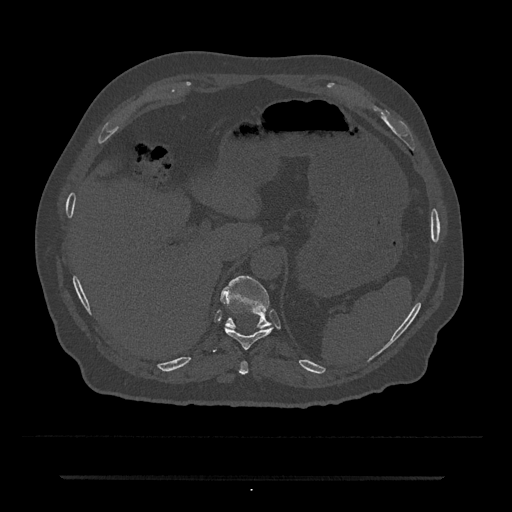
CT including the spine, one axial slice. Position 215 of 797 along the scan axis. Reconstruction kernel Br40s/3. 120 kVp. Bone window (W 1800 / L 400 HU). 0.5 mm slice thickness. 512 × 512 image matrix, field of view 437 × 437 mm. Patient: male, 69 years. From the clinical record (not read from this slice): primary cancer: prostate.
Structures marked on this image (semi-automatically segmented with operator editing):
- T10 vertebra: bounding box [x1, y1, x2, y2] px = [212, 326, 273, 352]
- T11 vertebra: [220, 275, 272, 329]
- T9 vertebra: [239, 361, 249, 375]